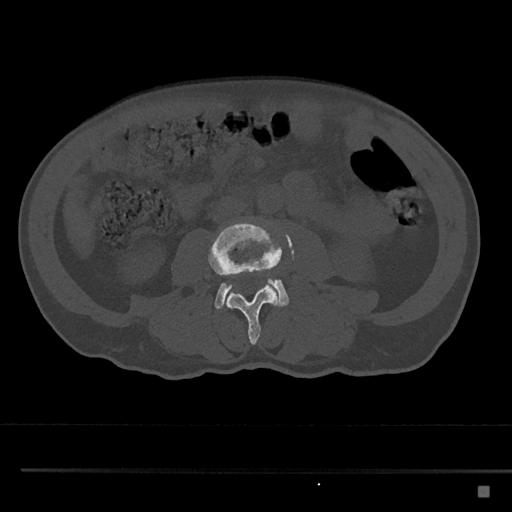
CT including the spine, one axial slice. Position 673 of 797 along the scan axis. 120 kVp. Bone window (W 1800 / L 400 HU). 0.5 mm slice thickness. 512 × 512 image matrix, field of view 391 × 391 mm. Male patient, age 59 years. Case-level facts recorded for this patient, not image findings: primary cancer: prostate.
Structures marked on this image (semi-automatically segmented with operator editing):
- L3 vertebra: box from (x=208, y=220) to (x=282, y=345) px
- L4 vertebra: (x=214, y=278)–(x=289, y=309)